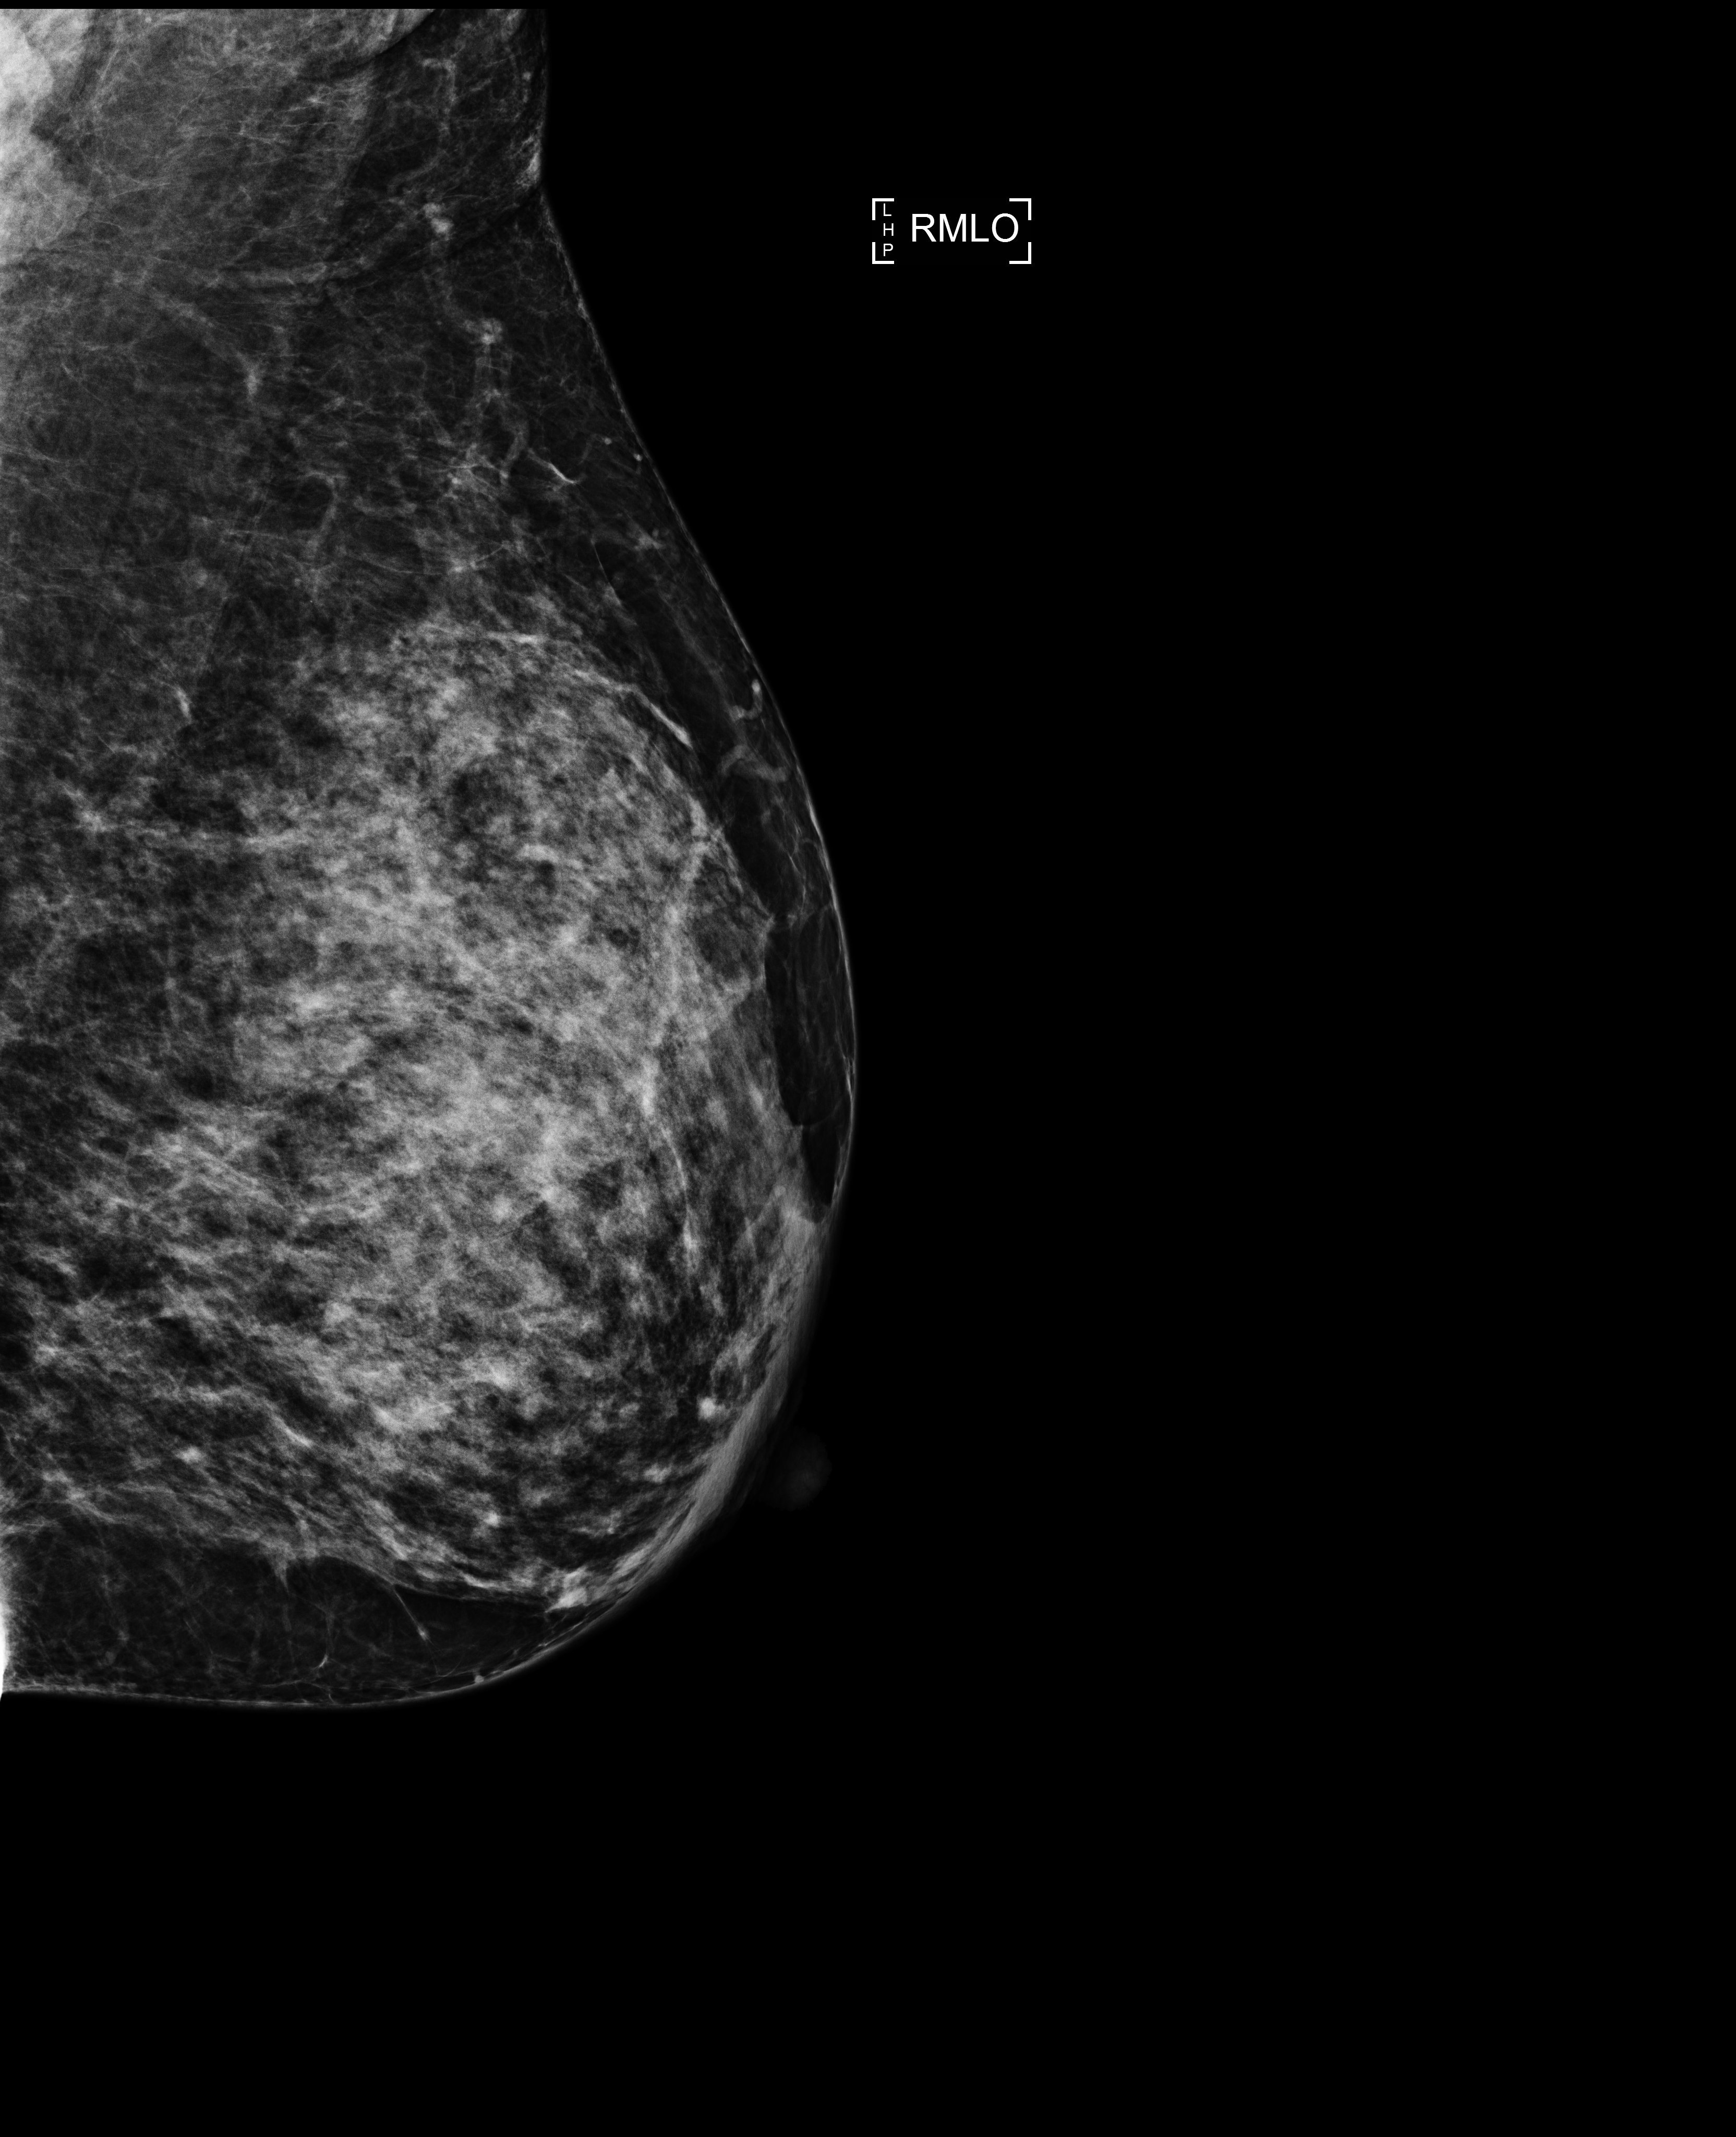
Annual screening mammography examination. Patient: female, 42 years.
Image type: full-field digital mammogram. Breast: right. Projection: medio-lateral oblique projection. Breast density at the screening exam (both breasts): heterogeneously dense (BI-RADS density category c). Final BI-RADS category for the screening round (tomosynthesis exam, both breasts): category 1. Recall: no recall after this screen.